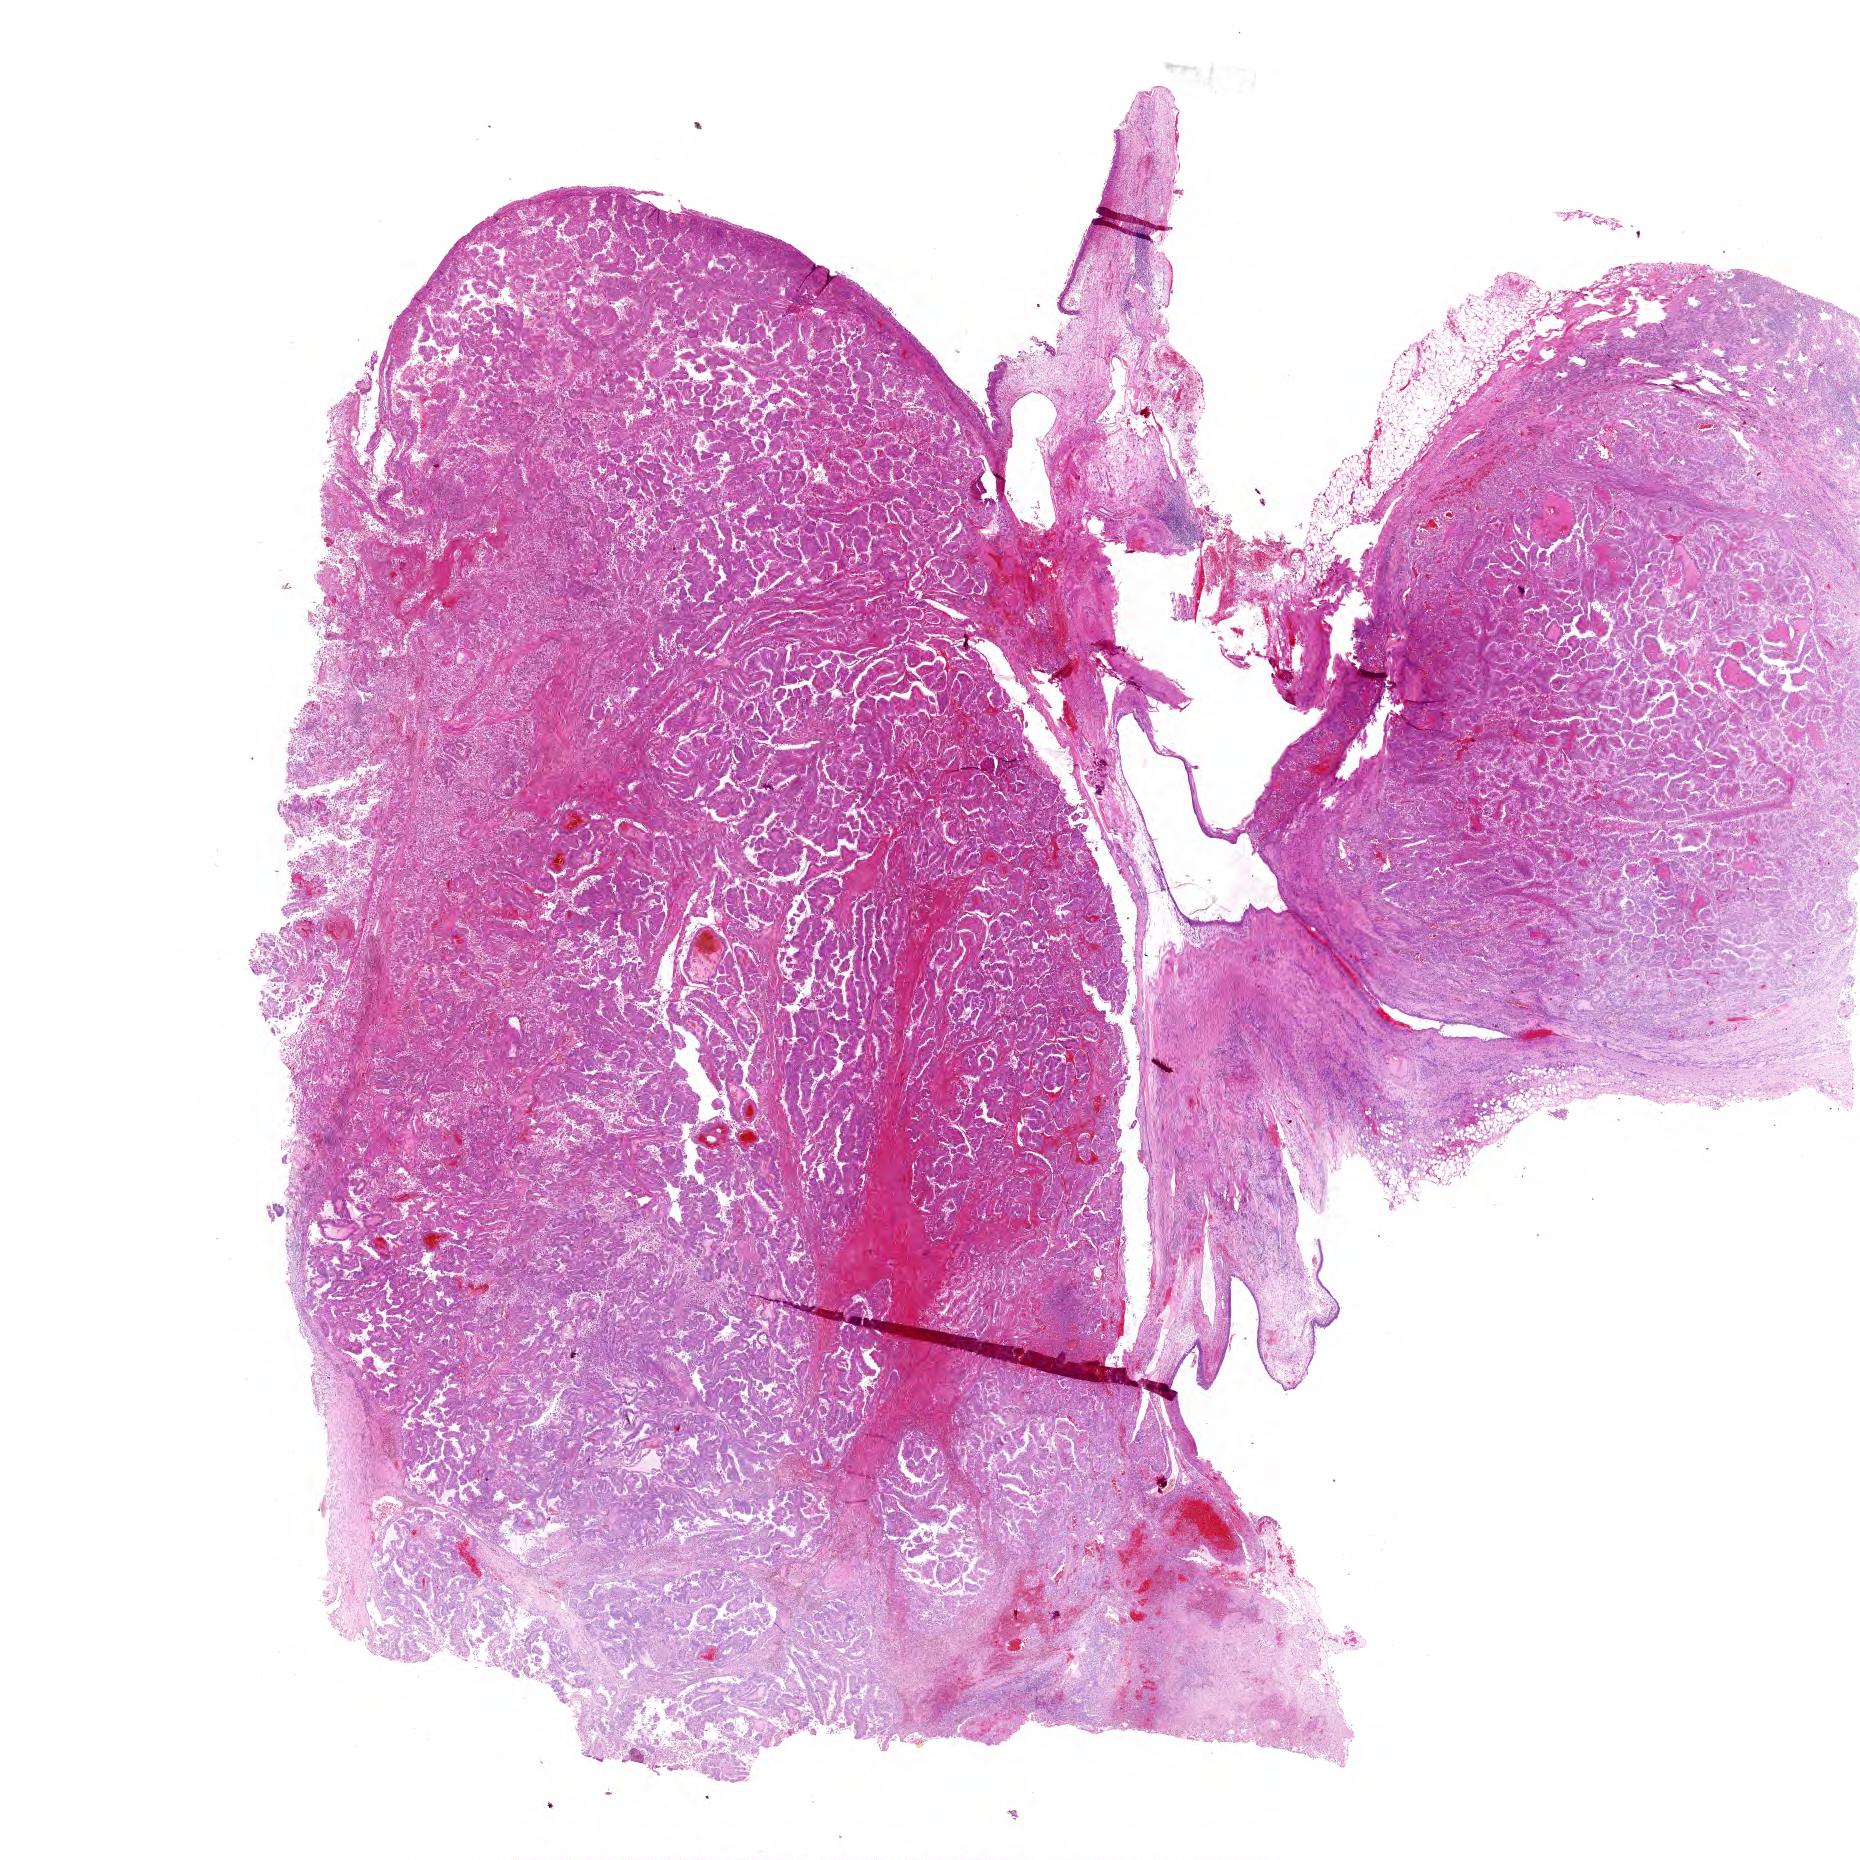
Whole-slide histology image, Hematoxylin and eosin (H&E) stained, shown as a low-resolution overview of the whole scanned area (about 23.2 x 23.2 mm, from a 40x scan); formalin-fixed paraffin-embedded (FFPE) diagnostic section; sample: primary tumour, kidney. Patient: female, age at initial diagnosis 59 years.
- lymph nodes positive (case pathology): 5 of 10 examined
- pathologic diagnosis: Papillary adenocarcinoma, NOS